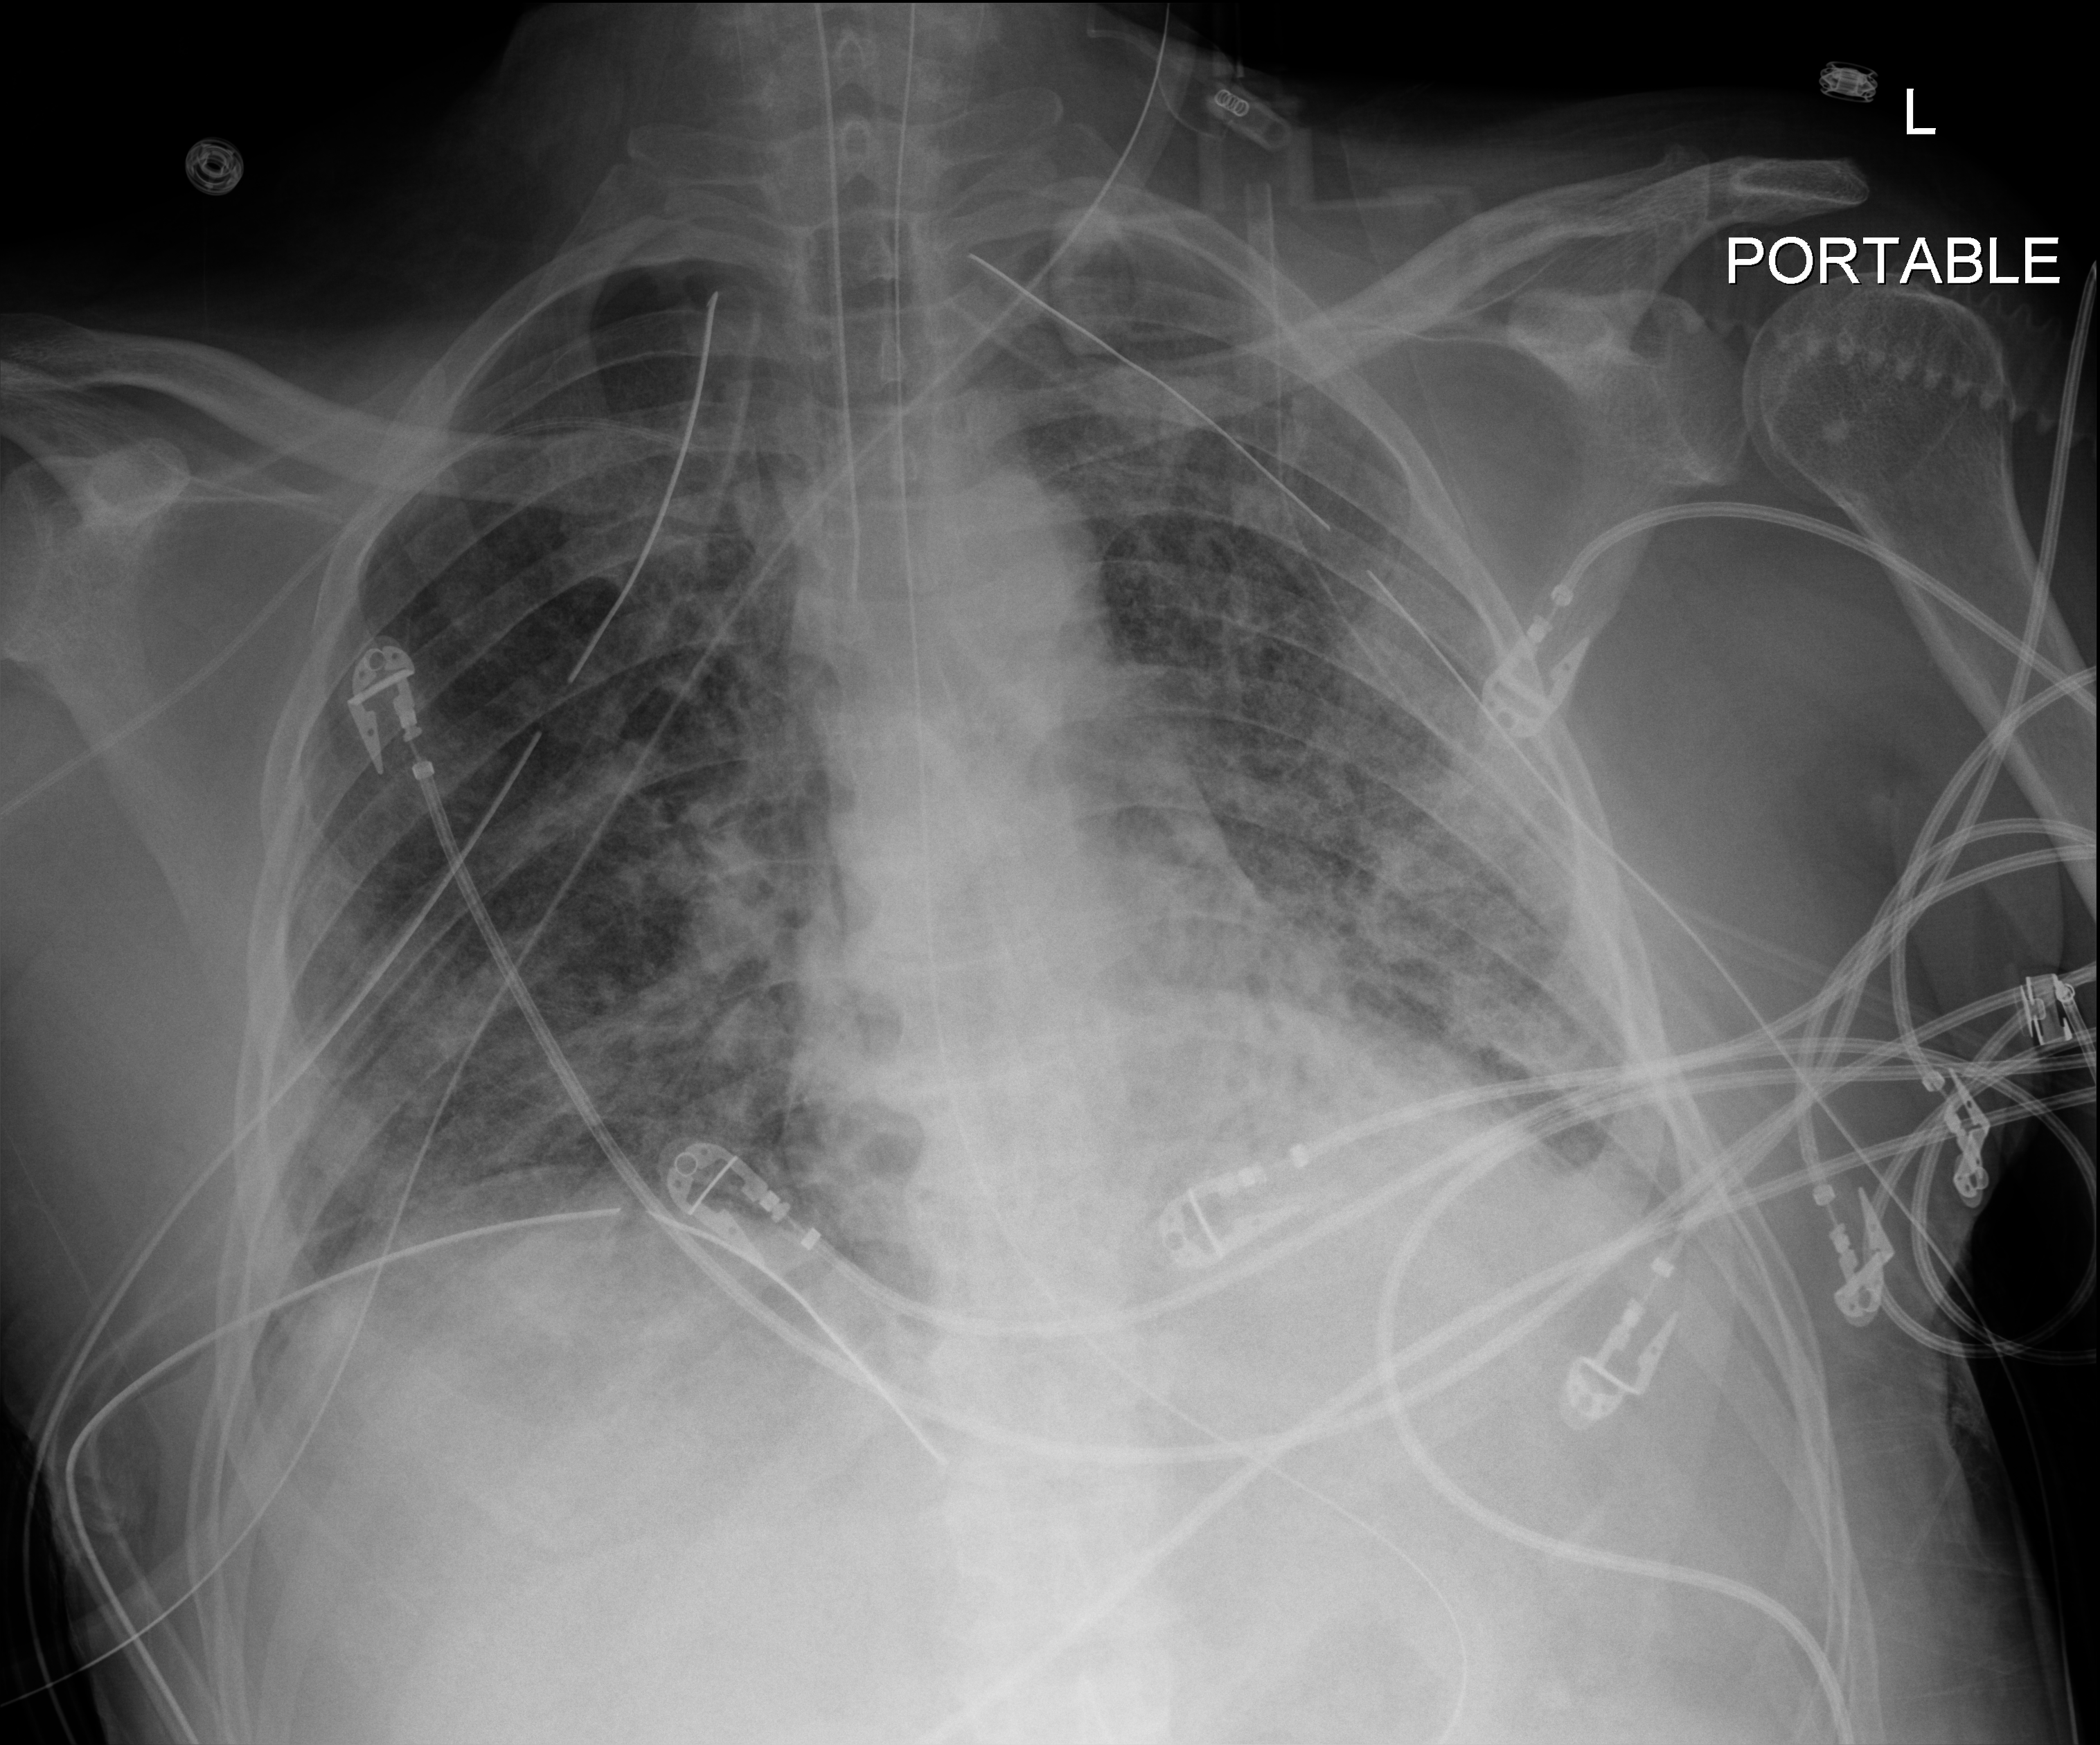
Bedside chest radiograph (digital radiography). Male patient hospitalised with COVID-19, age 18–59 years.
From the hospital-stay record, not from the radiograph (when in the stay this image was taken is not recorded): admitted to intensive care during this hospital stay: yes.